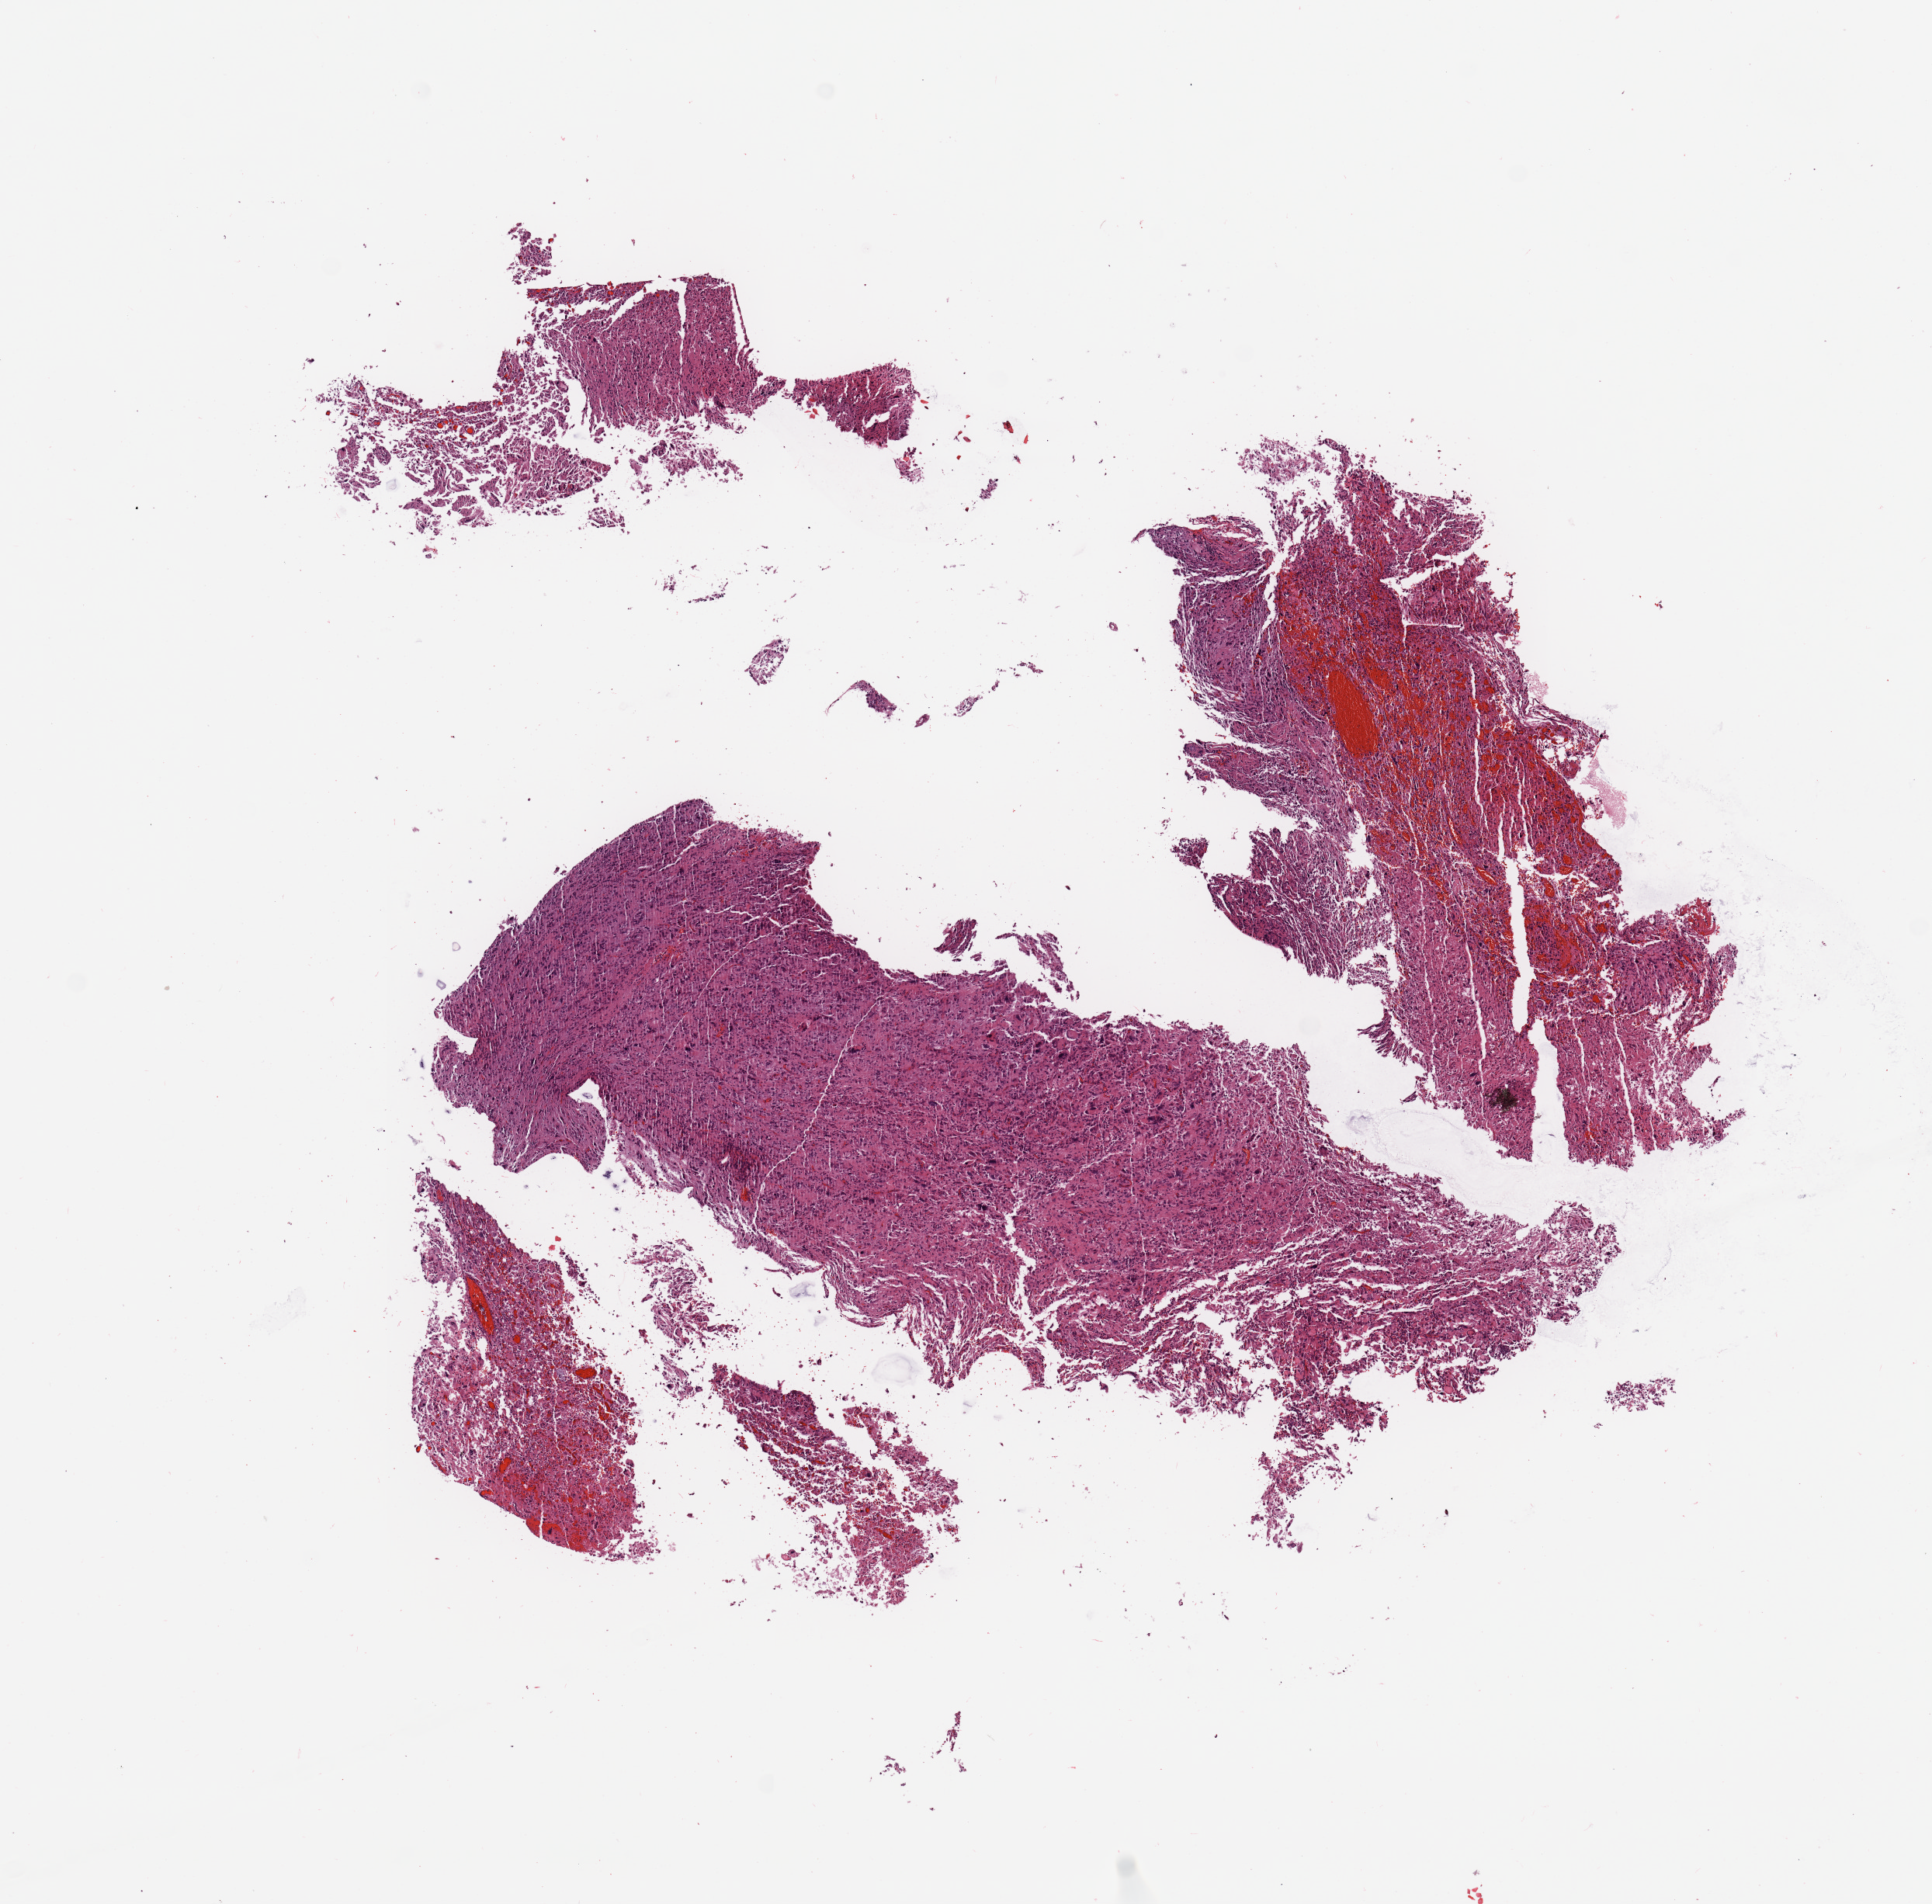
Digitized Hematoxylin and eosin (H&E) stained tissue section (whole slide) — whole scanned area (about 9.8 x 9.7 mm) shown as a low-resolution overview; tumour tissue sample, brain. Male, 50 y/o.
Diagnosis: Glioblastoma. Primary tumour site (as recorded): frontal lobe.